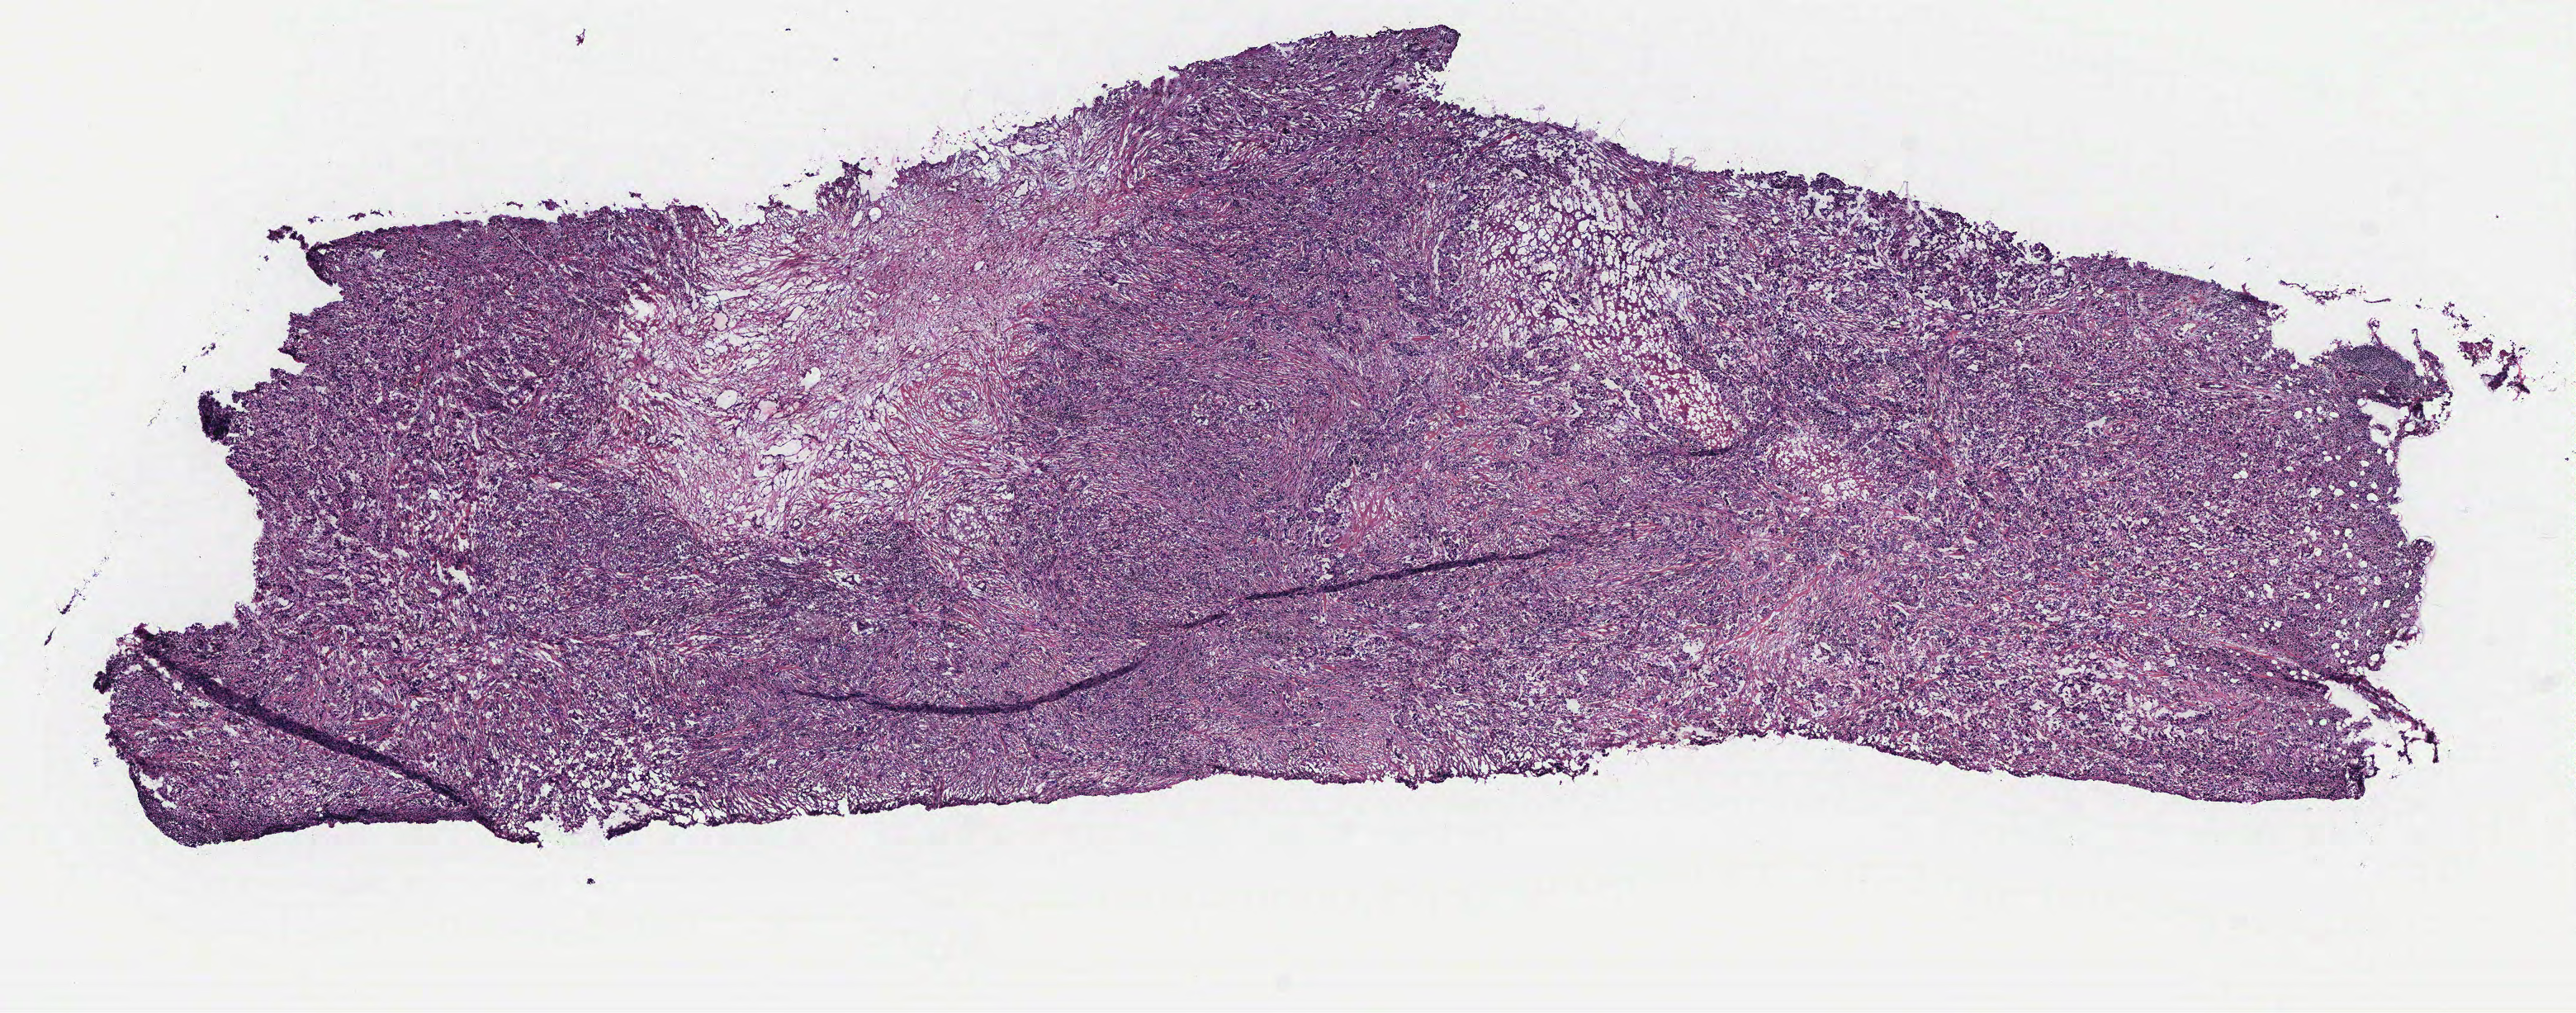
Hematoxylin and eosin (H&E) stained whole-slide image, low-resolution overview of the scanned area, about 12.5 x 4.9 mm (slide scanned at 40x); tumour tissue sample, breast. 70-year-old female patient.
- AJCC pathologic stage: IIB
- diagnosis: Infiltrating duct carcinoma, NOS